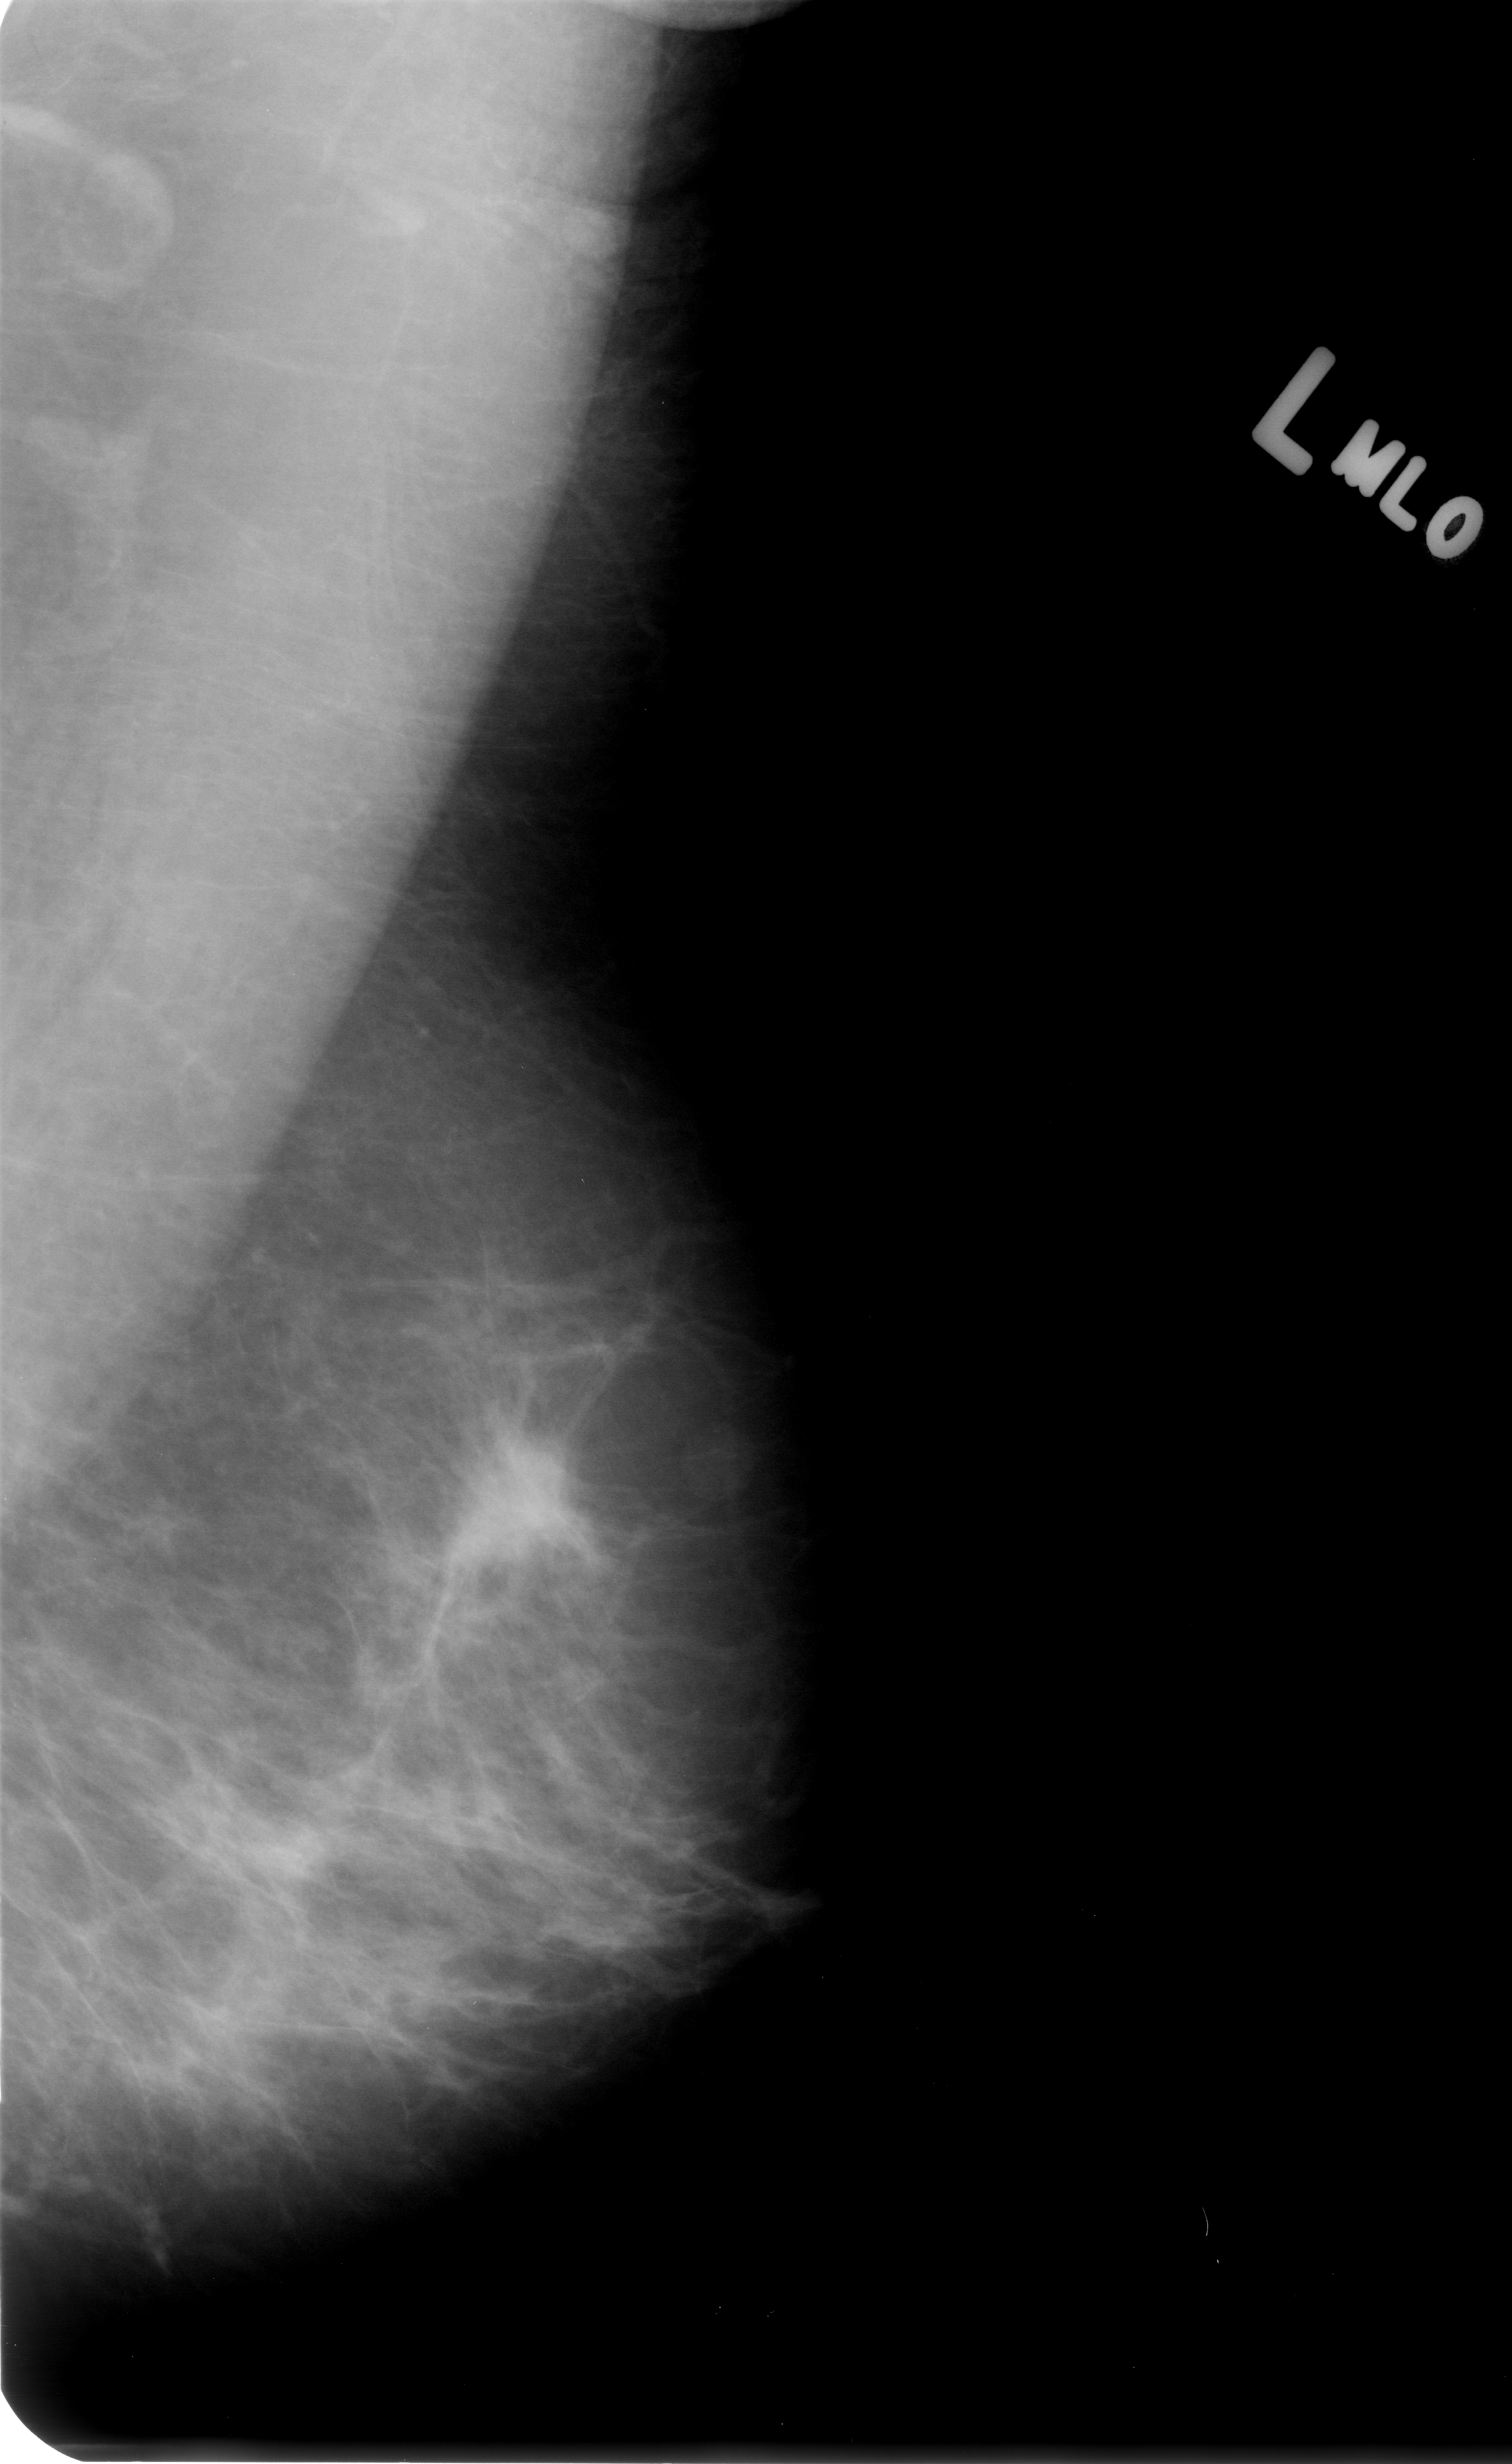
Scanned film-screen mammogram; left breast; mediolateral oblique (MLO) view; 1512 × 2464 image matrix.
Expert-marked regions of interest on this image (one box per marked abnormality):
- mass, shape irregular / architectural distortion, margins spiculated; BI-RADS assessment category 4; pathology (as recorded): malignant: bounding box <453,1418,605,1584> (left, top, right, bottom; pixels)